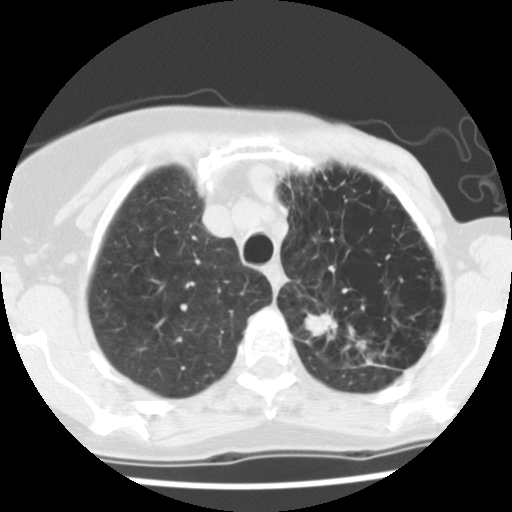
Chest CT (low-dose screening protocol), one axial image, baseline annual screen, lung window (W 1500 / L -600 HU), standard (soft-tissue) reconstruction kernel (STANDARD). Female participant, aged 67 years at enrolment.
- Expert reader's lesion annotation, box from (x=293, y=295) to (x=387, y=376) px.
- The screening reader recorded 2 non-calcified nodules or masses ≥4 mm on this exam (left upper lobe, left lower lobe); which of them this box marks is not recorded.
- Lung cancer was diagnosed 109 days after this screen: adenocarcinoma, NOS, left upper lobe, poorly differentiated (G3), stage IIB (AJCC 6th edition), 45 mm at pathology.